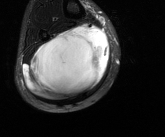
MRI of an extremity soft-tissue mass, one axial slice. Position 60 of 81 along the scan axis. T2-weighted fat-saturated. MR volume resampled by the dataset authors to the PET/CT grid (not the native acquisition matrix). 165 × 137 image matrix, field of view 161 × 134 mm. Male patient. Case-level facts recorded for this patient, not image findings: histological type: liposarcoma - round cell; grade: high; site of the primary tumour: right calf.
Annotated regions visible in this slice (expert contour drawn on MRI and transferred to this co-registered scan by the dataset authors):
- gross tumour volume (mass): bounding box (x1, y1, x2, y2) in pixels: (23, 23, 109, 101)